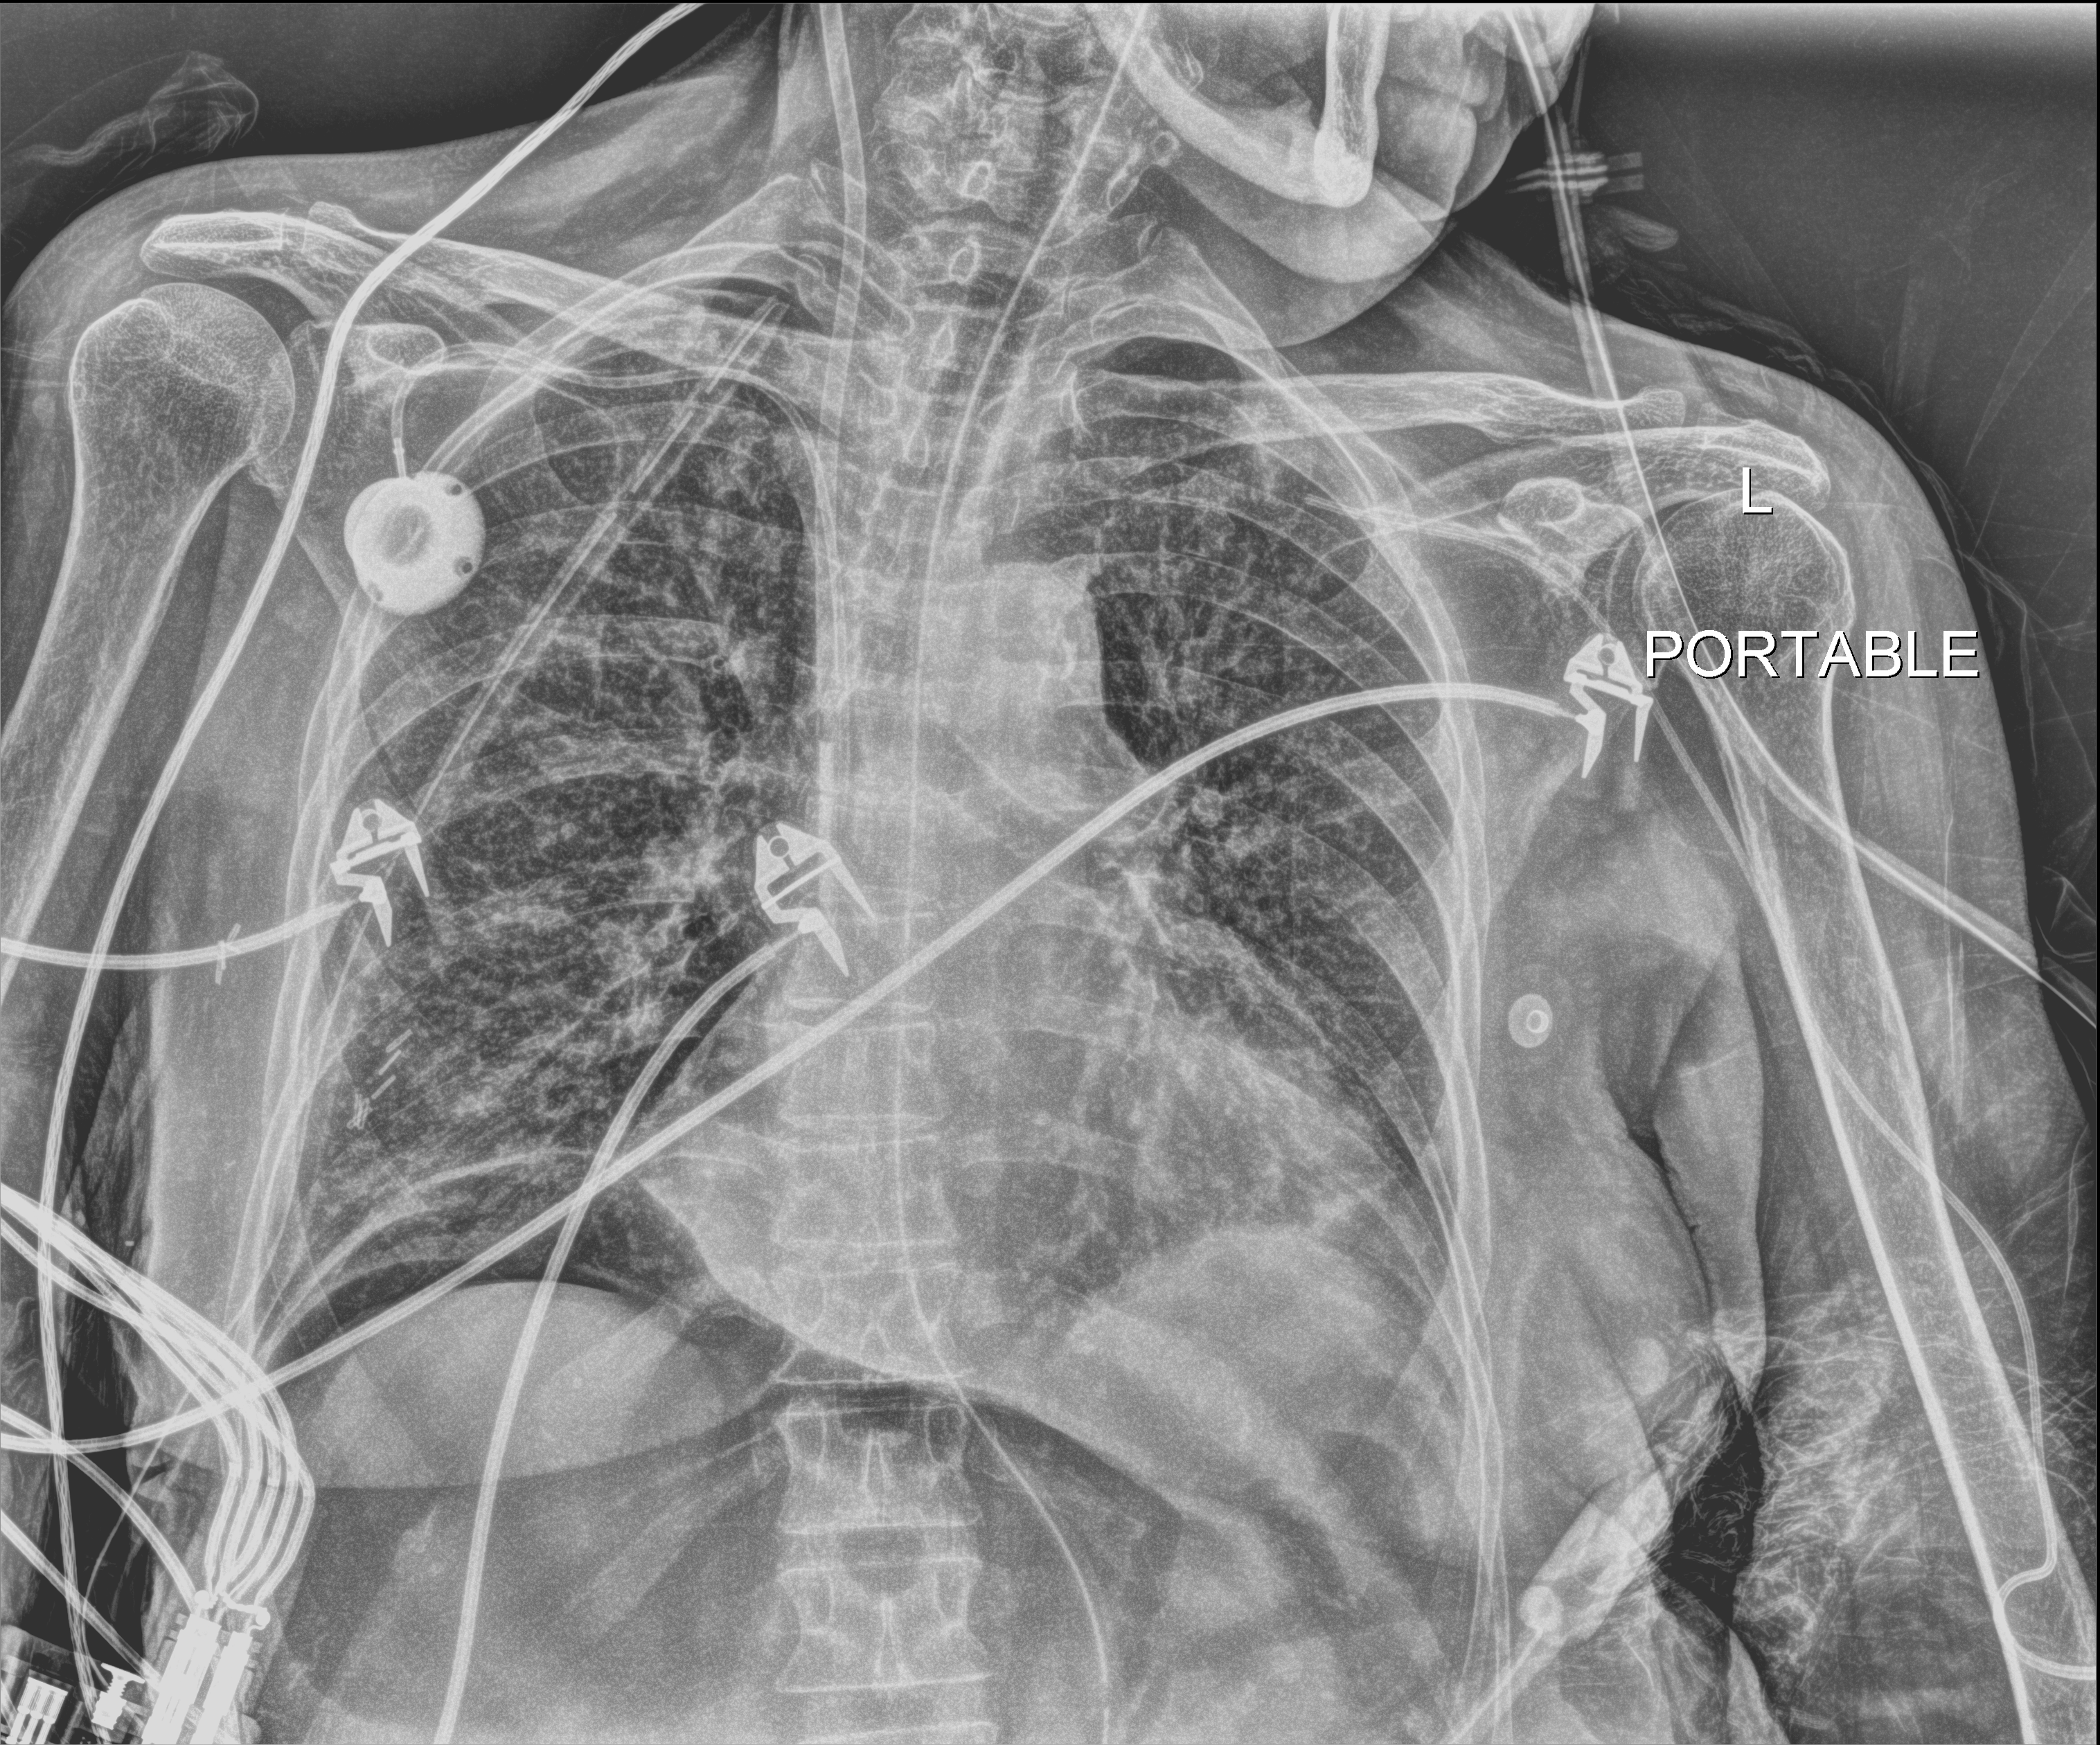
Chest X-ray (portable), anteroposterior (AP) projection. Patient hospitalised with COVID-19; female, aged 60–74 years.
Admission-level facts for this patient (not findings on this image; timing relative to this image not recorded): admitted to intensive care during this hospital stay: yes; mechanically ventilated during this hospital stay: yes; hypertension (admission record): yes.